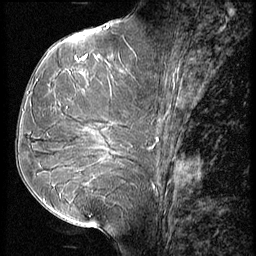
Breast MRI (dynamic contrast-enhanced), one sagittal slice. Position 30 of 56 along the scan axis. 3 images stored at this slice position (order not interpretable as contrast timing). 1.5 T. TE 4.2 ms, TR 9 ms. 256 × 256 image matrix. Patient: female, 51 years. From the clinical record (not read from this slice): setting: breast cancer imaged before/during neoadjuvant chemotherapy; receptor status: HR-positive, HER2-negative.
Annotated regions visible in this slice (semi-automatically segmented with operator editing):
- analysis volume of interest (the breast-tissue region the enhancement analysis was run in; not a lesion): bounding box <23,56,156,165> (left, top, right, bottom; pixels)
- tumour enhancement mask (voxels above the 140 % enhancement threshold inside the analysis volume of interest): <81,56,89,75>